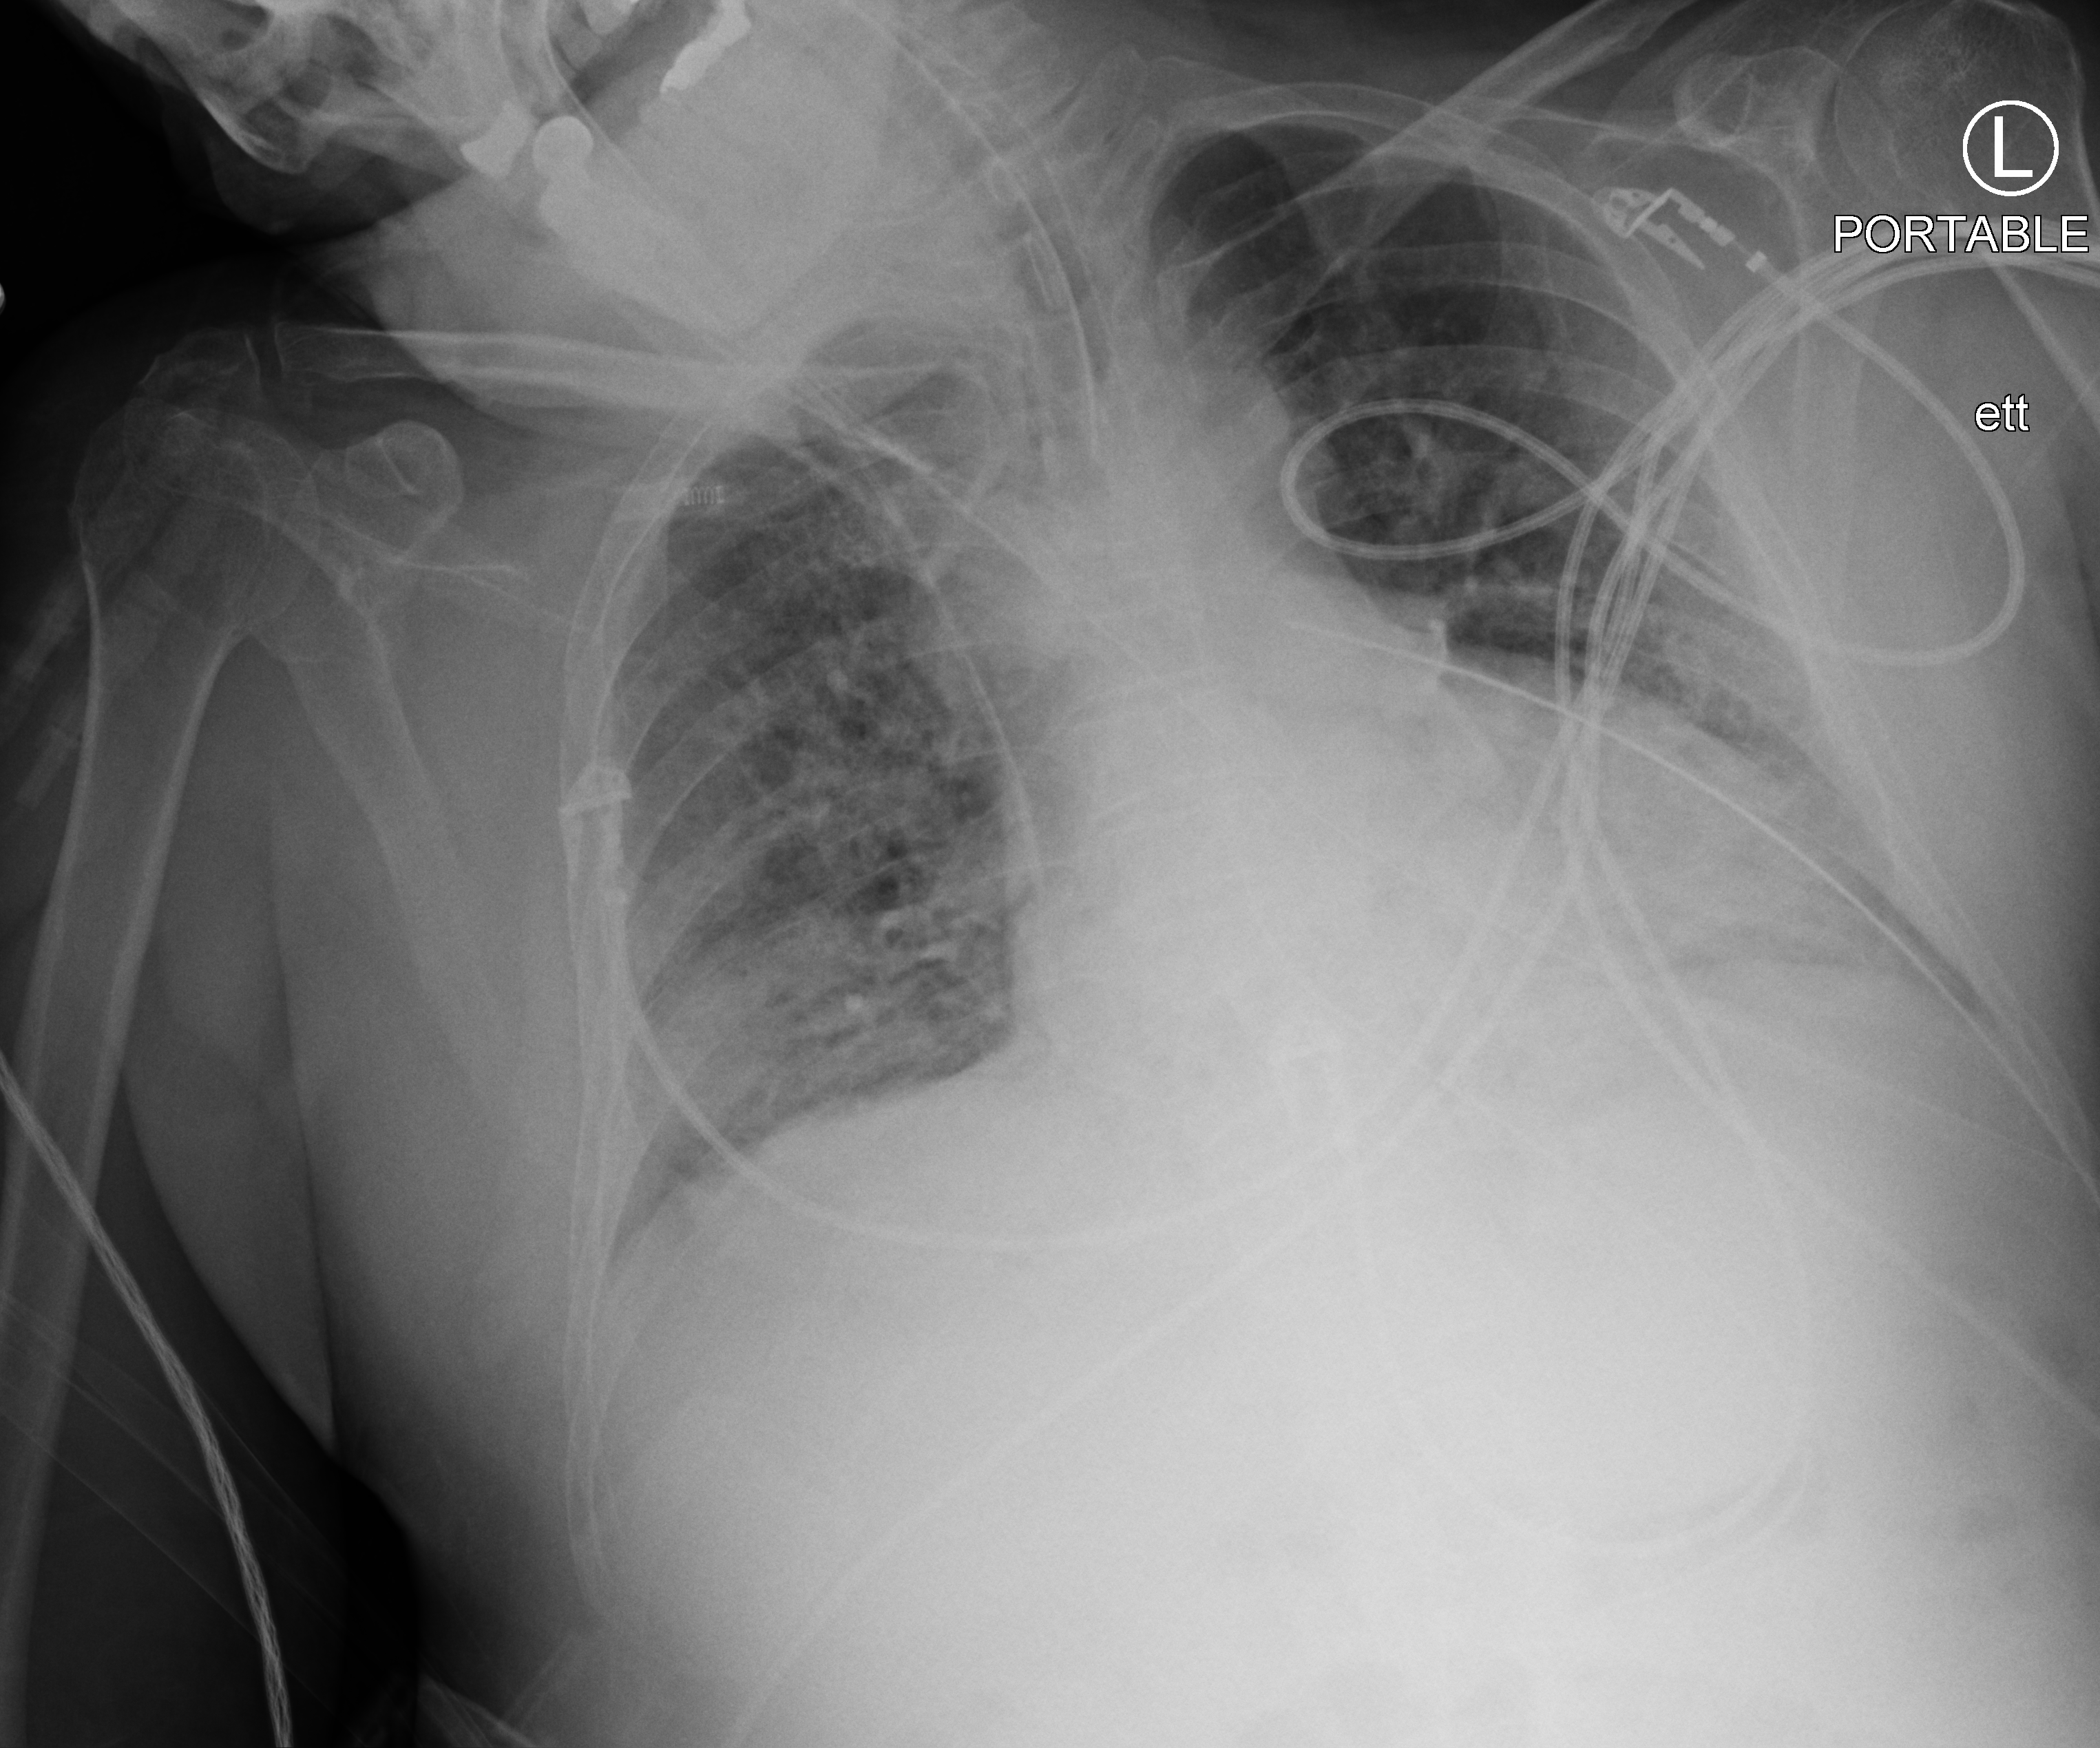
Portable chest radiograph; anteroposterior (AP) projection. Male patient hospitalised with COVID-19, age 60–74 years.
From the hospital-stay record, not from the radiograph (when in the stay this image was taken is not recorded): mechanically ventilated during this hospital stay: yes.